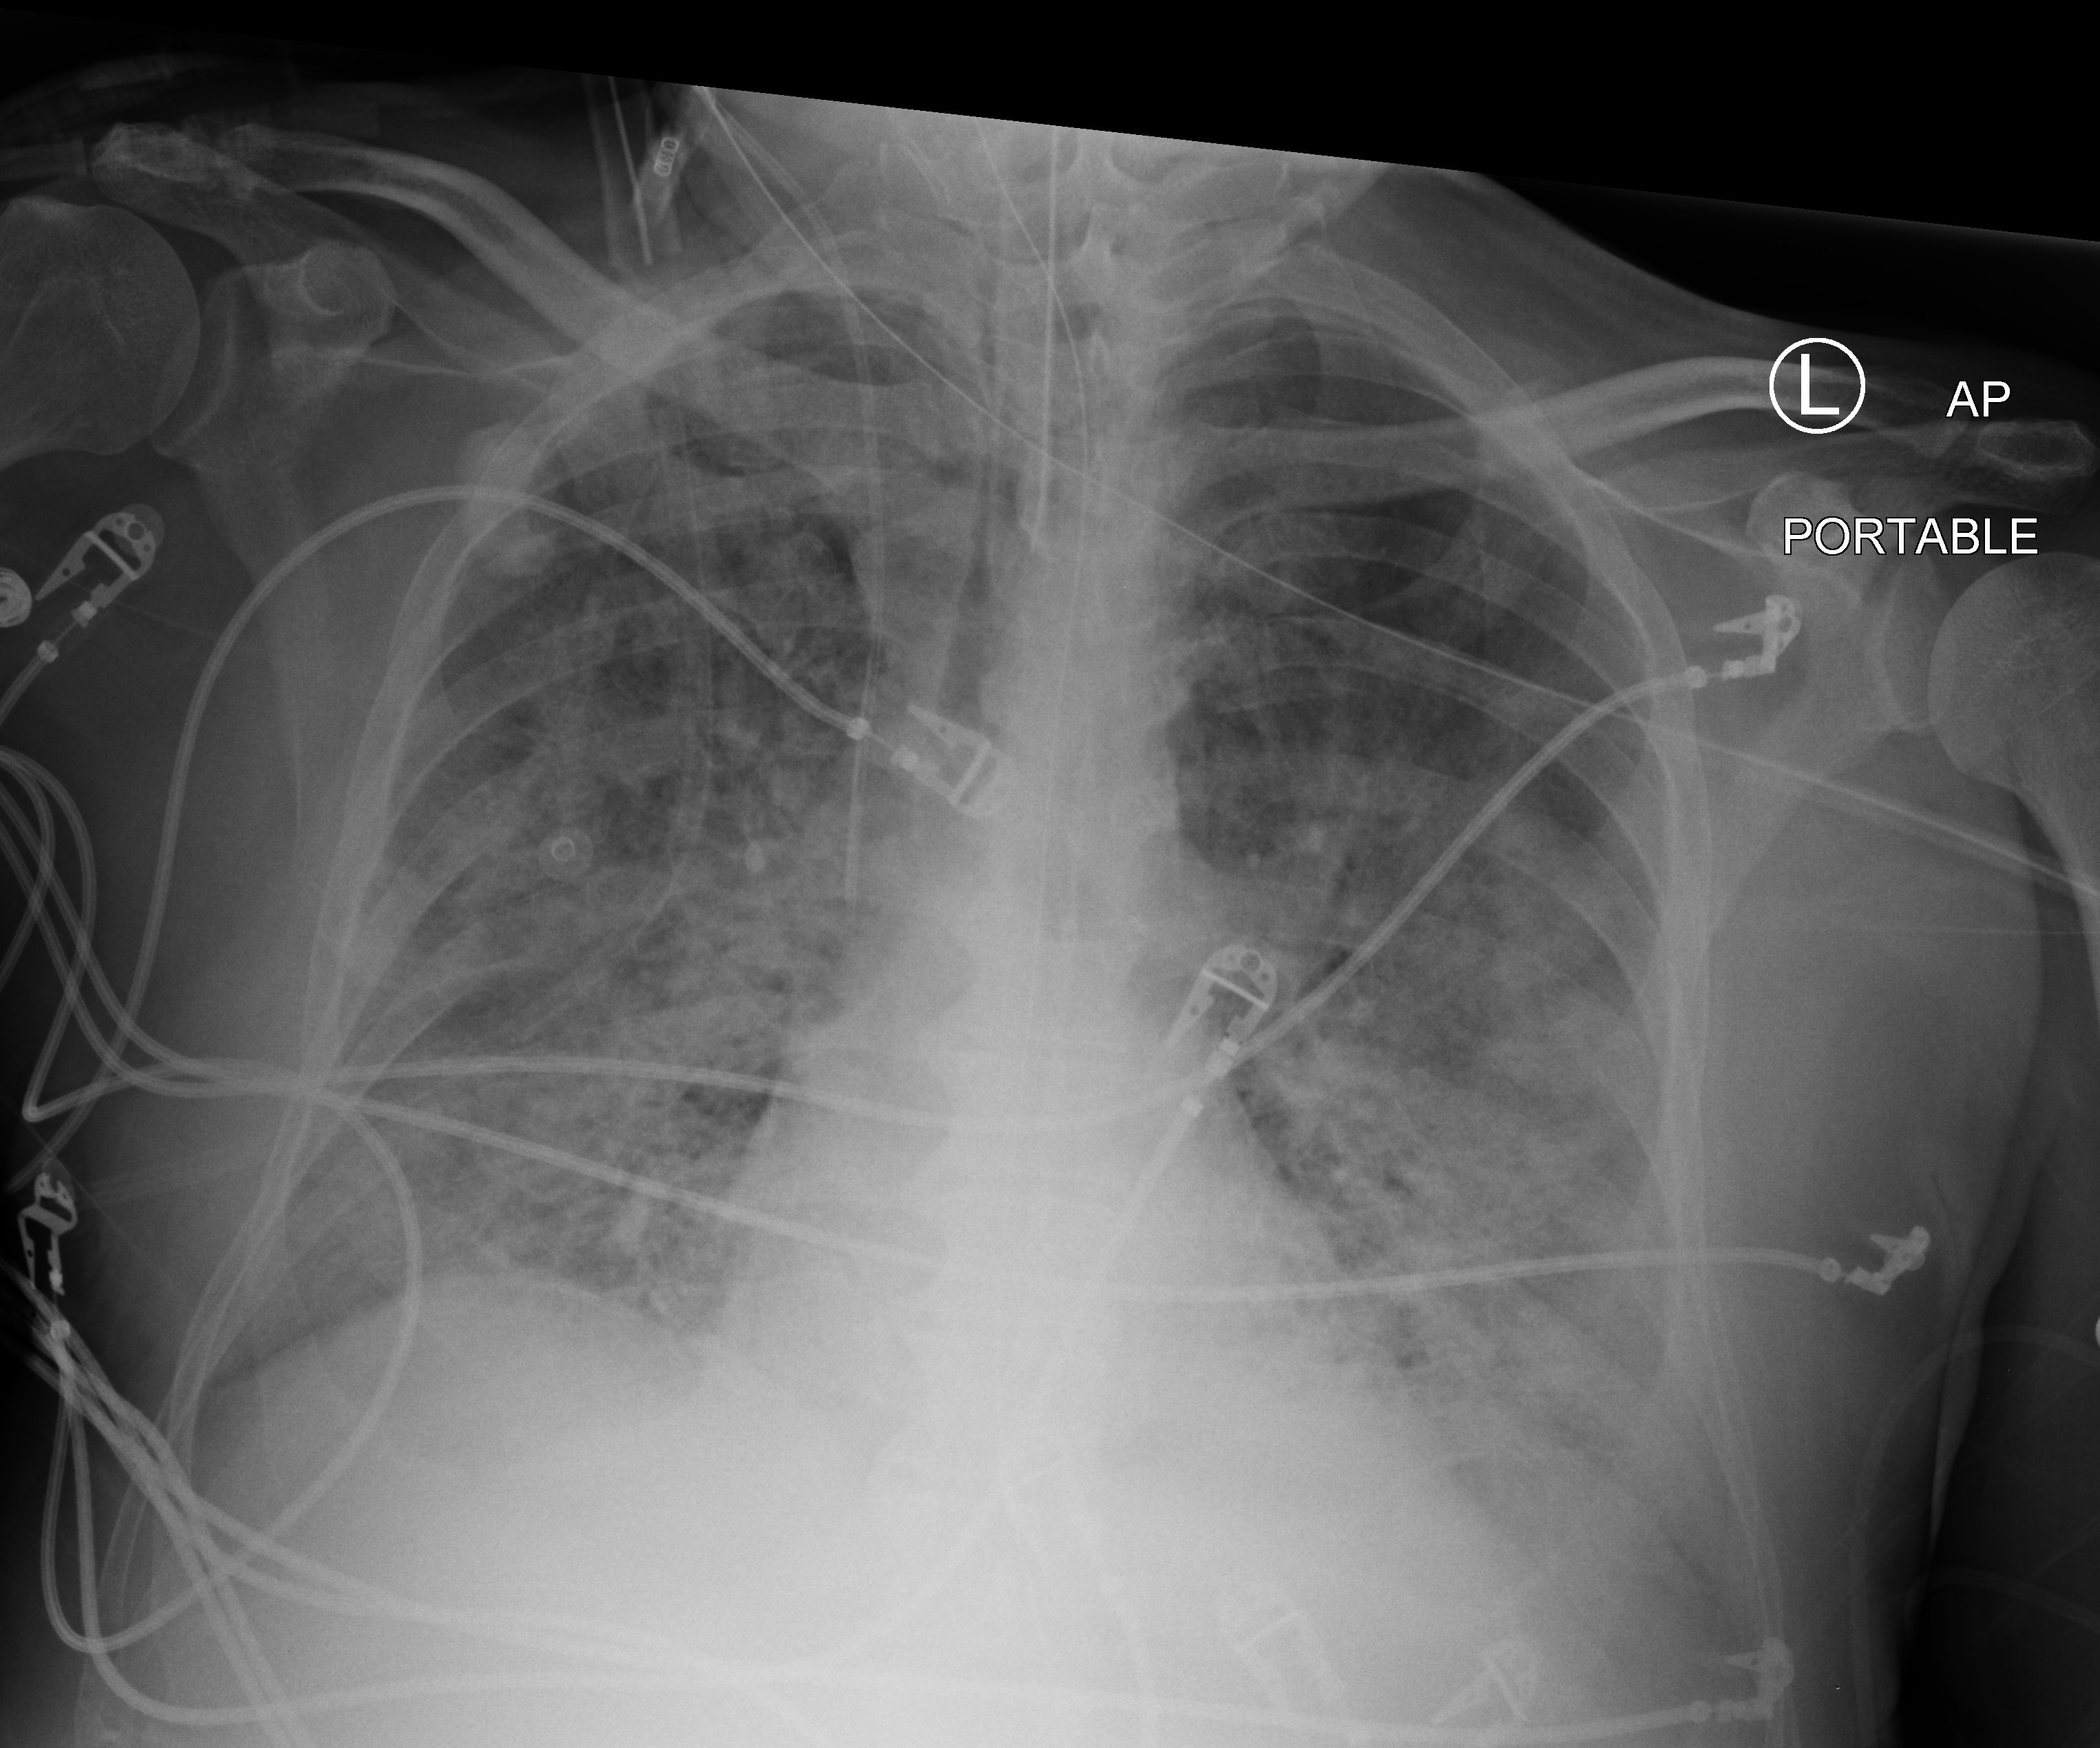
Chest X-ray (portable). Male patient hospitalised with COVID-19, age 60–74 years.
From the hospital-stay record, not from the radiograph (when in the stay this image was taken is not recorded):
- mechanically ventilated during this hospital stay: yes
- hypertension (admission record): no
- admitted to intensive care during this hospital stay: yes